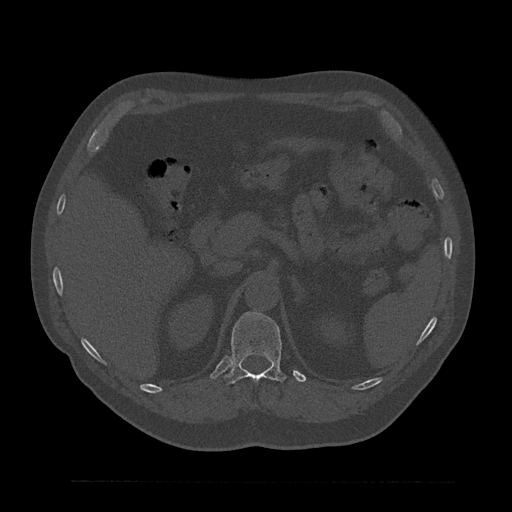
CT including the spine, one axial slice. Slice 231 of 797 in the series (ordered by position). Reconstruction kernel Br40s/3. Bone window (W 1800 / L 400 HU). 512 × 512 image matrix, field of view 430 × 430 mm. Male patient, age 61 years. Case-level facts recorded for this patient, not image findings: primary cancer: prostate.
Annotated regions visible in this slice (semi-automatically segmented with operator editing):
- T12 vertebra: bounding box <225,312,287,384> (left, top, right, bottom; pixels)